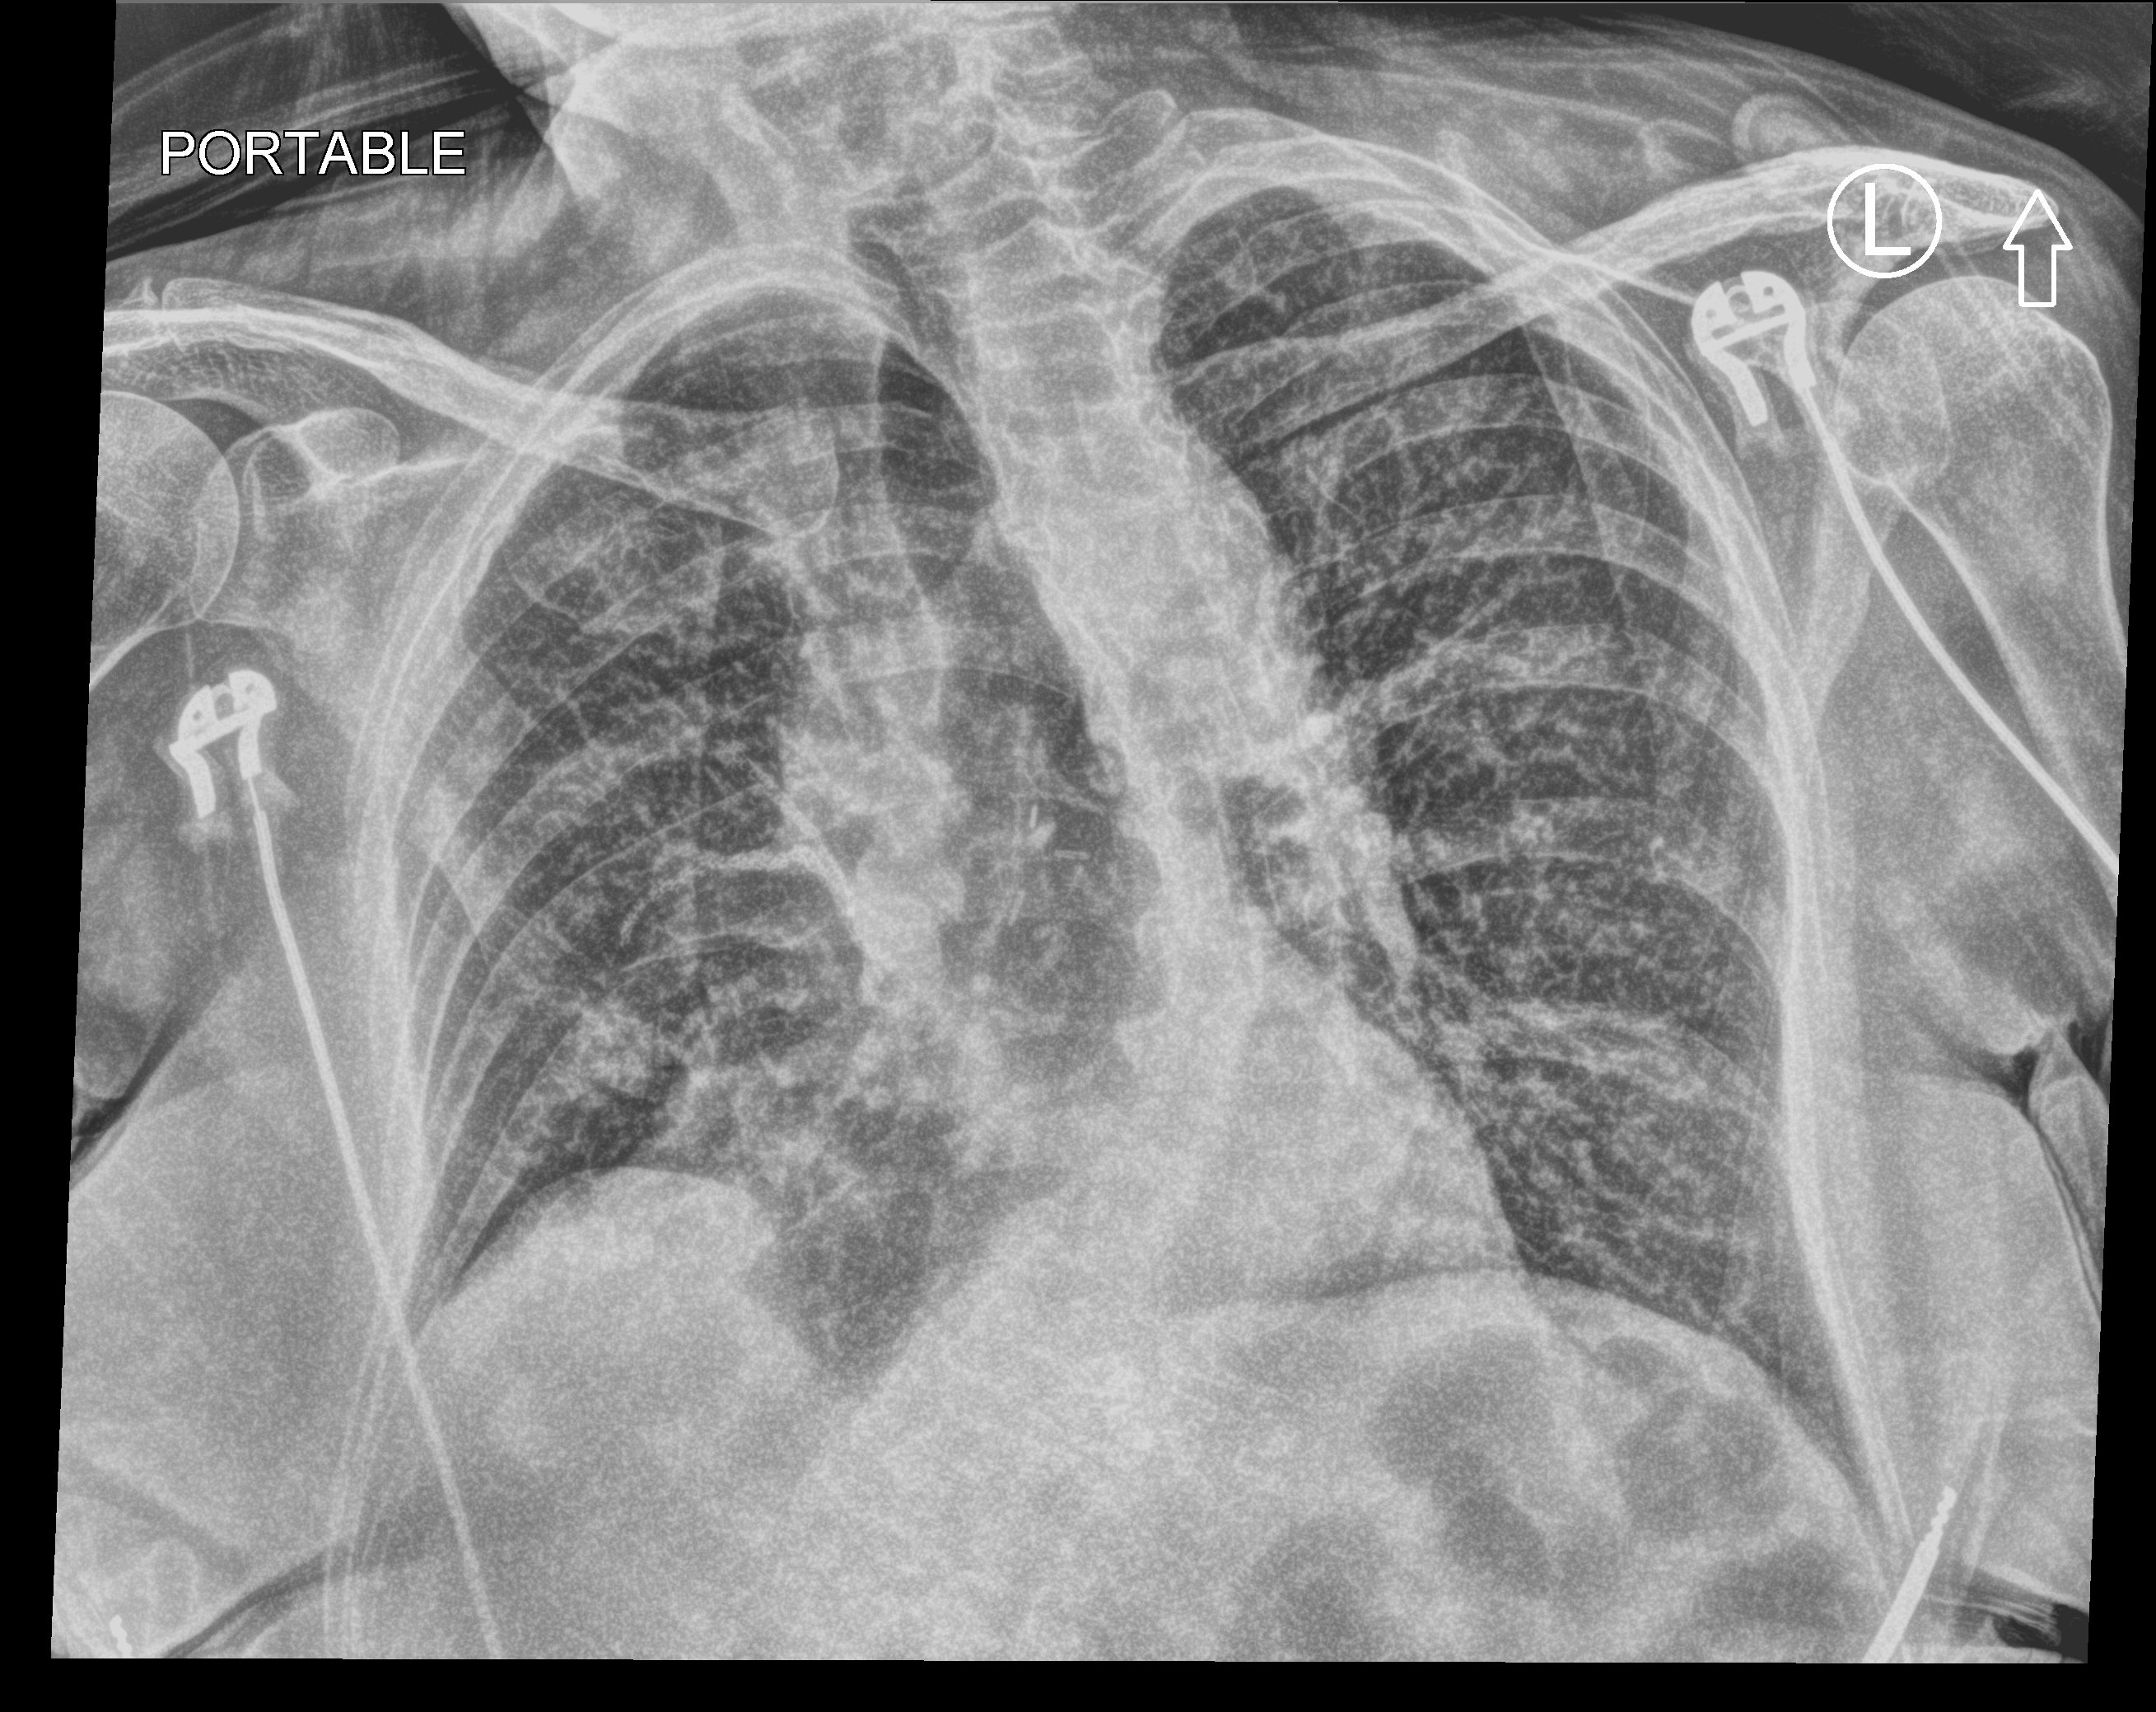
Portable chest radiograph, anteroposterior (AP) projection. Patient hospitalised with COVID-19; female, aged 75–90 years.
Admission-level facts for this patient (not findings on this image; timing relative to this image not recorded): admitted to intensive care during this hospital stay: no.